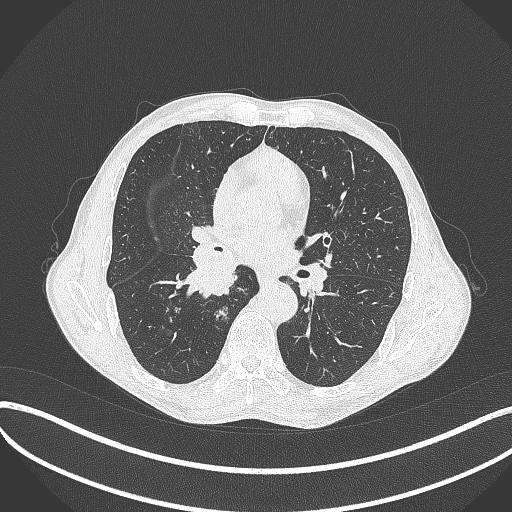
Chest CT, one axial slice. 120 kVp. Lung window (W 1500 / L -600 HU). 1 mm slice thickness. 512 × 512 image matrix, field of view 400 × 400 mm. Male patient, age 65 years. From the clinical record (not read from this slice): clinical TNM (as recorded): T2a N0 M0; histopathological grade: G2.
Outlined on this slice (rectangle marked by the reading radiologist):
- lung tumour (recorded histology: squamous cell carcinoma): bounding box [x1, y1, x2, y2] px = [178, 230, 243, 307]